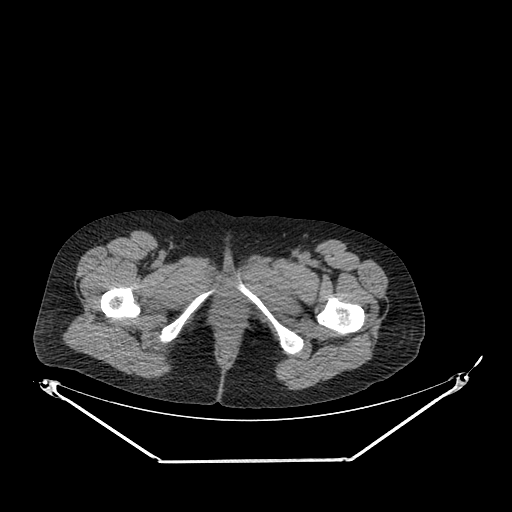
CT of an extremity soft-tissue mass (from a PET/CT study), one axial slice. Position 258 of 267 along the scan axis. Reconstruction kernel SOFT. 120 kVp. Soft-tissue window (W 400 / L 40 HU). 3.75 mm slice thickness. 512 × 512 image matrix. Female patient. Case-level facts recorded for this patient, not image findings: histological type: pleiomorphic leiomyosarcoma; grade: intermediate; site of the primary tumour: left thigh.
Structures marked on this image (expert contour drawn on MRI and transferred to this co-registered scan by the dataset authors):
- gross tumour volume including surrounding oedema: bounding box (x1, y1, x2, y2) in pixels: (247, 267, 270, 280)